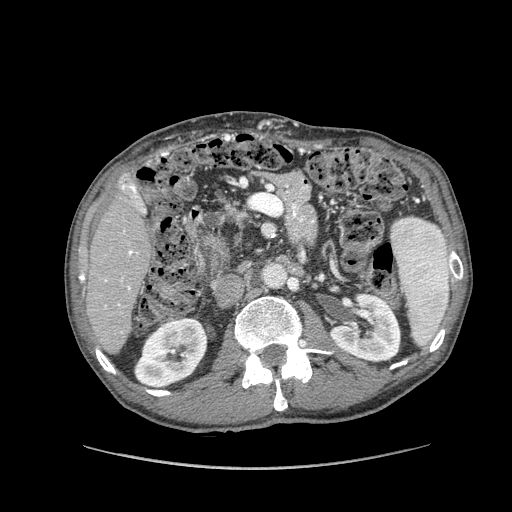
Contrast-enhanced abdominal CT (liver protocol), one axial slice. Slice 39 of 162 in the series (ordered by position). Reconstruction kernel STANDARD. Soft-tissue window (W 400 / L 40 HU). 2.5 mm slice thickness. 512 × 512 image matrix. From the clinical record (not read from this slice): diagnosis: hepatocellular carcinoma (patient treated with transarterial chemoembolisation; whether this scan precedes or follows treatment is not stated here); TNM stage (as recorded): Stage-IIIA; Child-Pugh class: A; tumour size: 9.9 cm.
Annotated regions visible in this slice (semi-automatically segmented with operator editing):
- liver parenchyma outside the tumour (the mass and vessels are separate outlines, so this box may not span the whole liver): bounding box <86,172,150,352> (left, top, right, bottom; pixels)
- liver vessels: <105,184,145,308>